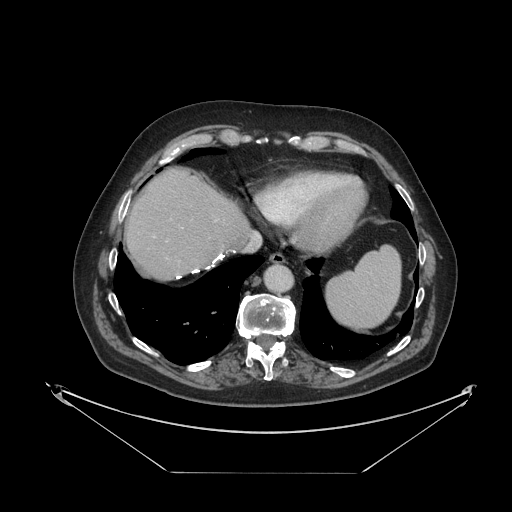
Contrast-enhanced abdominal CT, one axial slice; position 104 of 121 along the scan axis; 120 kVp; intravenous contrast given; soft-tissue window (W 400 / L 40 HU); 2.5 mm slice thickness; 512 × 512 image matrix, field of view 500 × 500 mm. Male patient, age 68 years. From the clinical record (not read from this slice): diagnosis: colorectal cancer liver metastases, imaged before liver resection; multiple liver metastases: no; largest metastasis: 4 cm; disease in both lobes: no.
Structures marked on this image (outlined manually by an expert reader):
- liver: bounding box [x1, y1, x2, y2] px = [127, 170, 249, 279]
- planned liver remnant (the part of the liver to remain after resection): [127, 170, 249, 279]